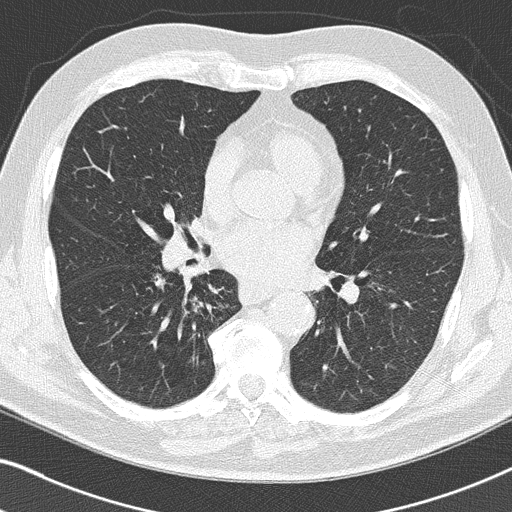
Chest CT (low-dose screening protocol), one axial image. Third annual screen. Lung window (W 1500 / L -600 HU). Slice 90 of 155 in the series. 512 × 512 image matrix. Male, age 66 years at enrolment. Current smoker at enrolment.
- Expert reader's lesion annotation, box from (x=139, y=264) to (x=230, y=327) px.
- Screening reader's record for this exam (one nodule recorded; not confirmed to be the boxed lesion): non-calcified nodule or mass ≥4 mm, right upper lobe, 5 × 4 mm, smooth margins, pre-existing on the prior screen: yes; interval growth: no.
- Later outcome: lung cancer diagnosed 38 days after this screen — squamous cell carcinoma, NOS, right lower lobe, poorly differentiated (G3), stage IIA (AJCC 6th edition), 22 mm at pathology.